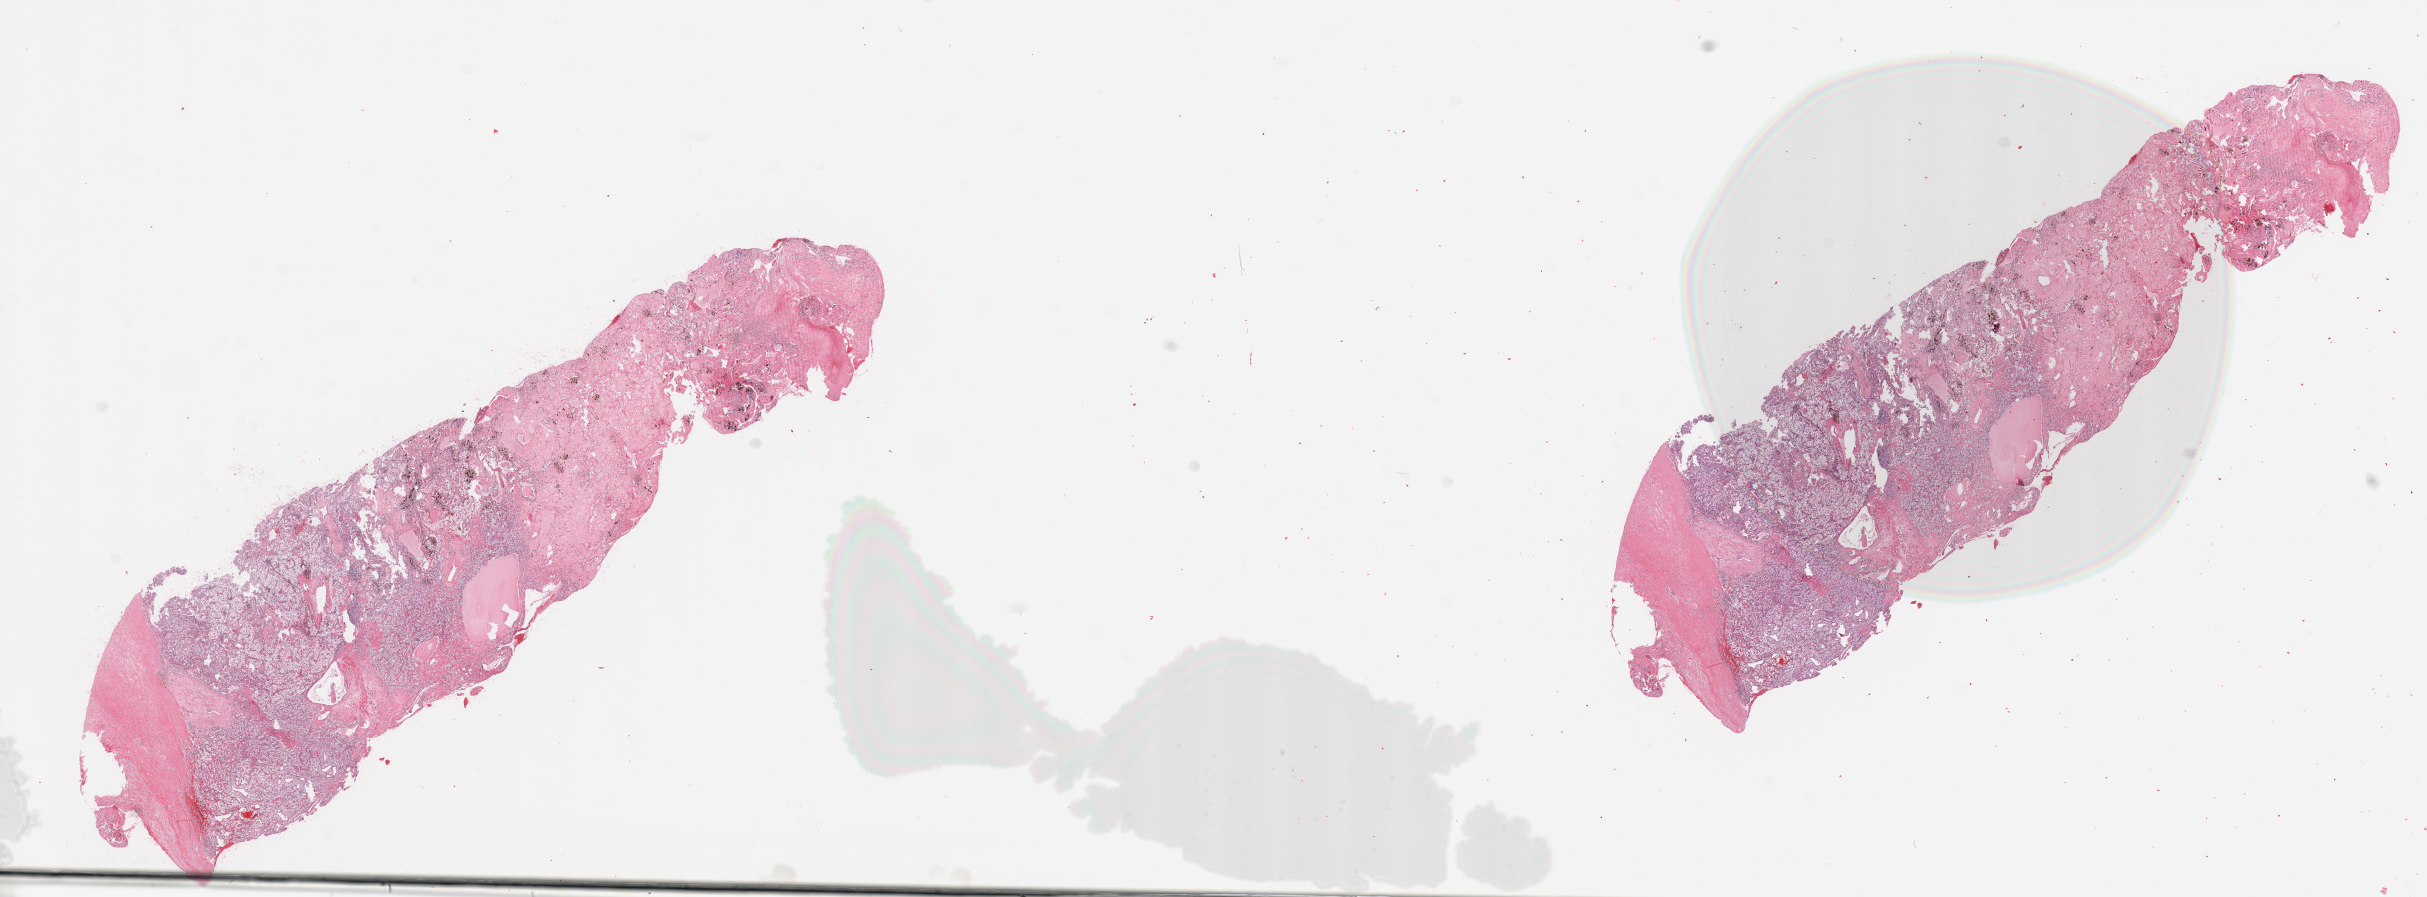
Whole-slide histology image, Hematoxylin and eosin (H&E) stained, a low-resolution overview of the entire scanned area, about 38.4 x 14.2 mm (acquisition: 20x scan), kidney, tumour tissue. Patient: male, age 57 years. Histologic grade: G3 (poorly differentiated).
- AJCC pathologic stage: III
- diagnosis: Renal cell carcinoma, NOS